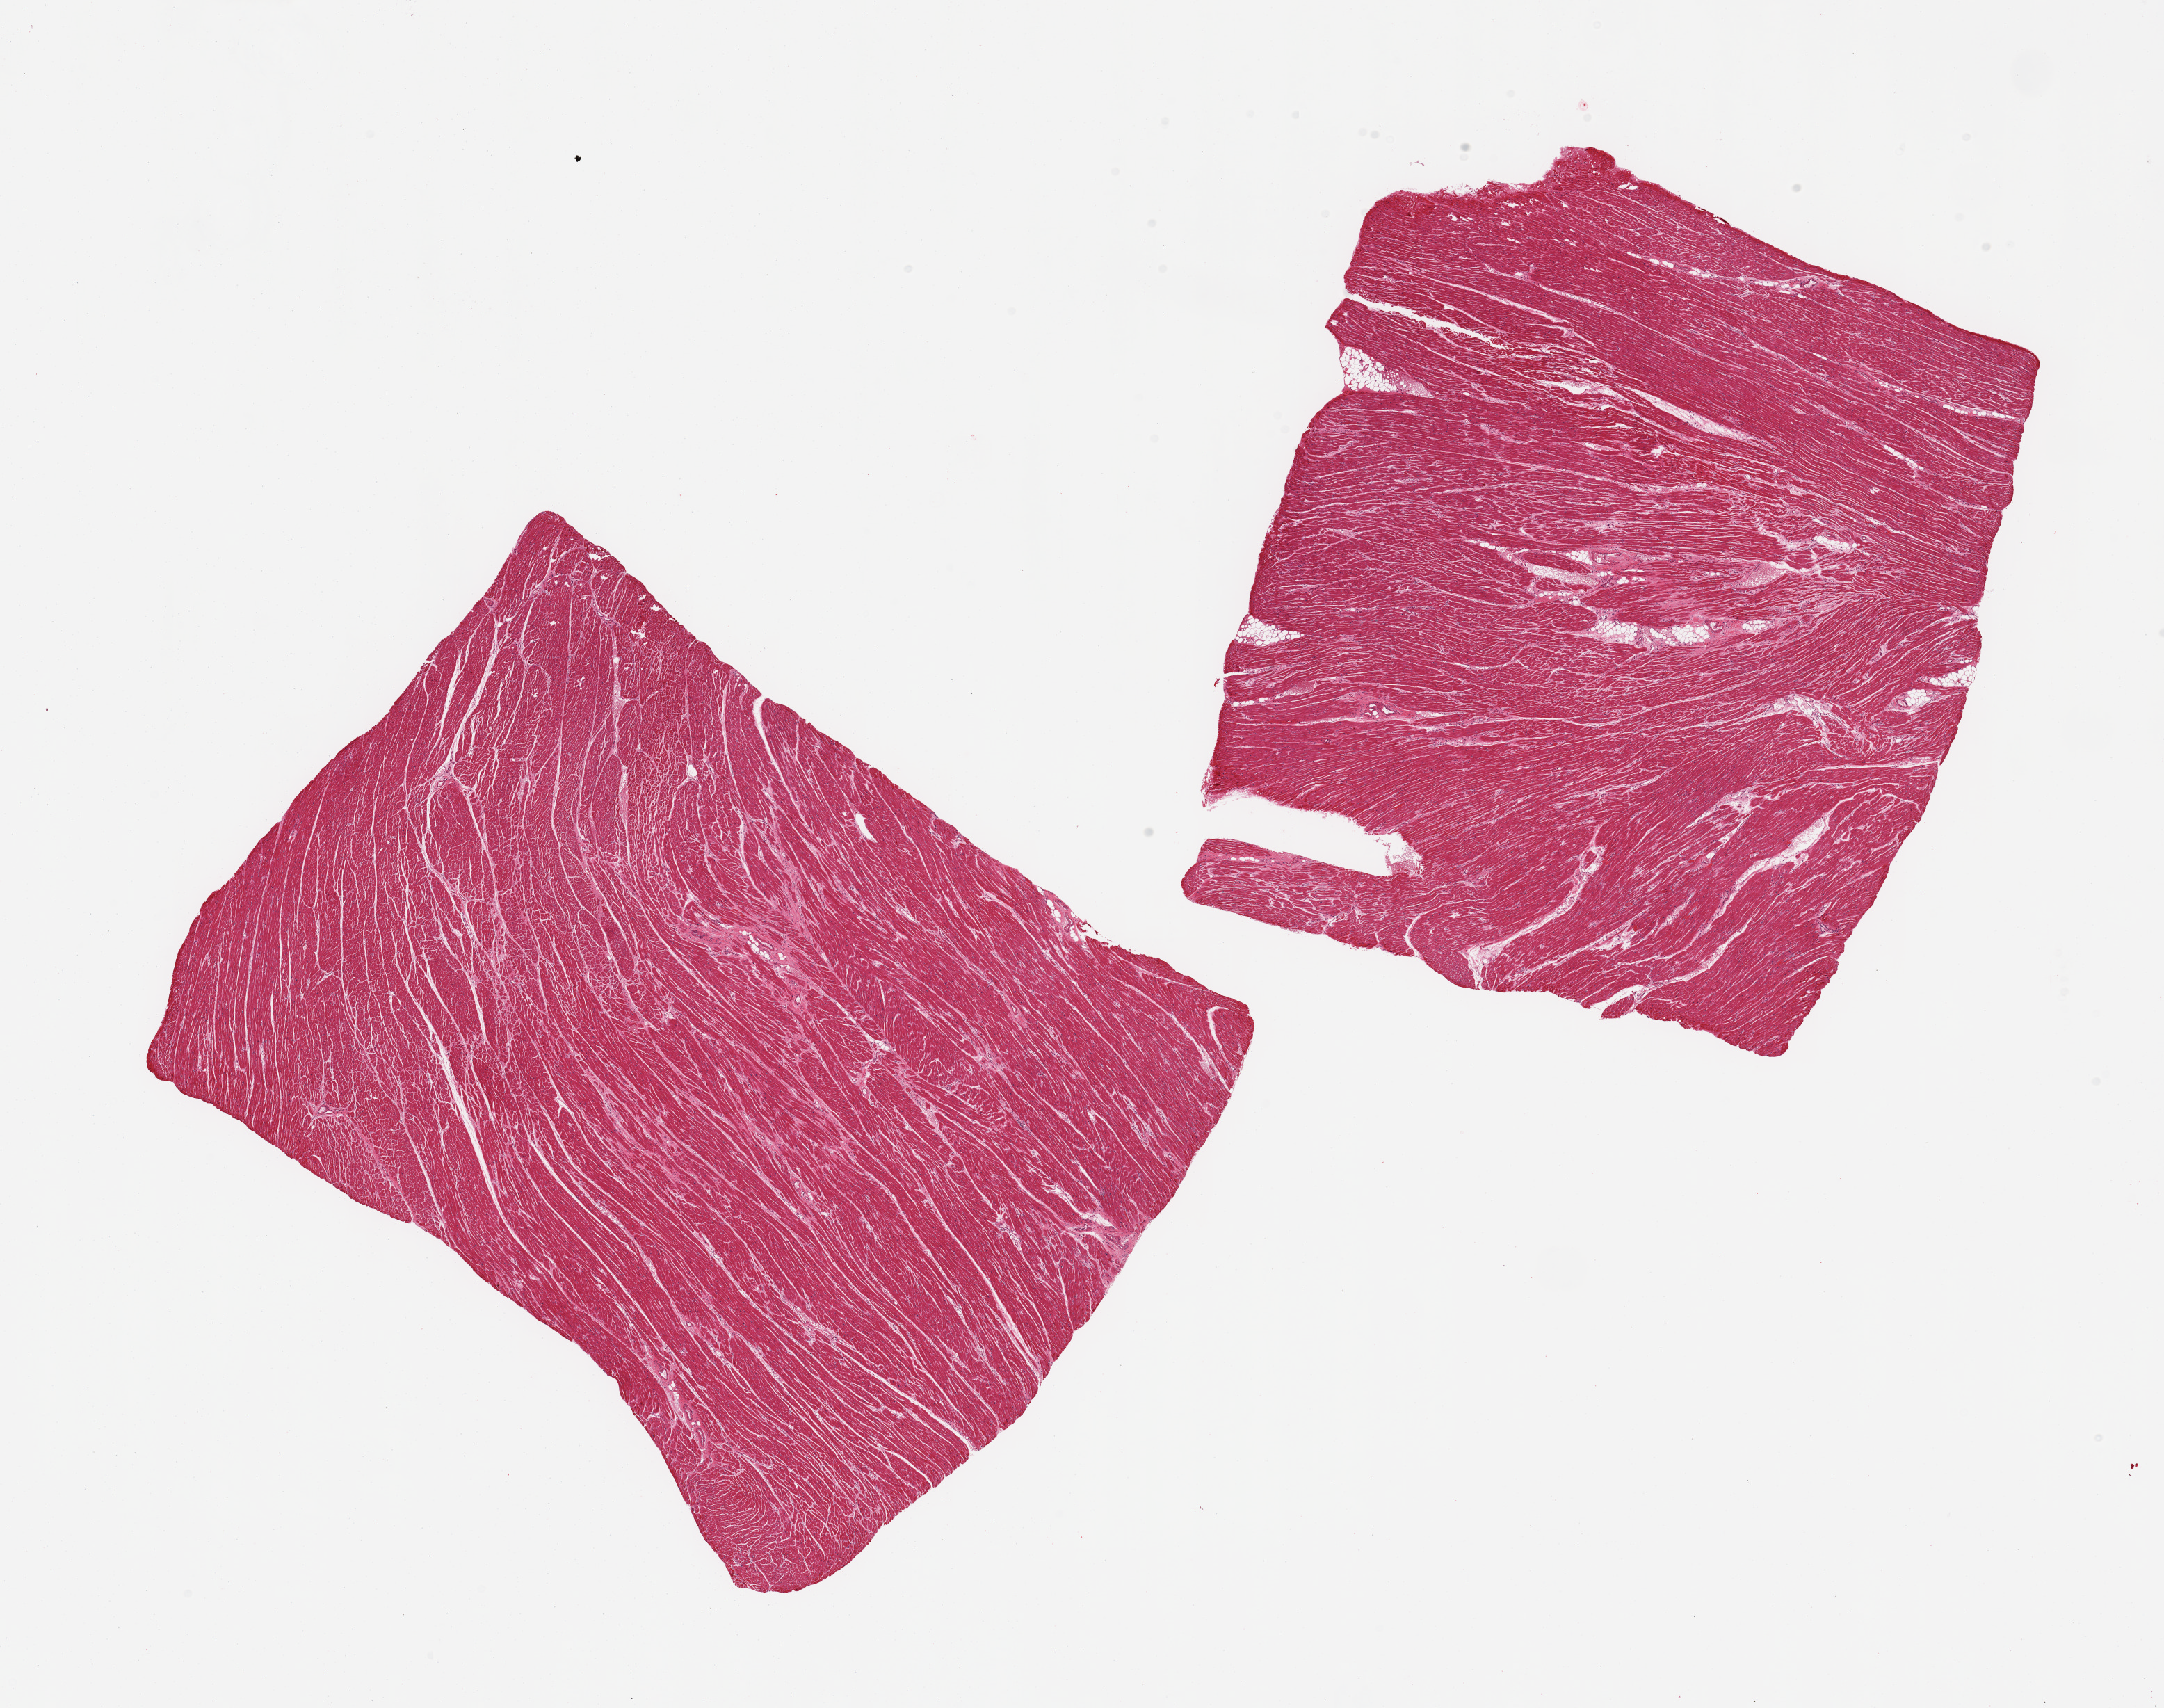
Haematoxylin and eosin whole-slide image, brightfield — low-resolution overview of the scanned area, about 24.6 x 19.4 mm (from a 20x scan). PAXgene-fixed, paraffin-embedded tissue. Section of heart (target tissue). Donor tissue sample.
• review note (as recorded): 2 pieces, mild chronic ischemic change/interstitial fibrosis